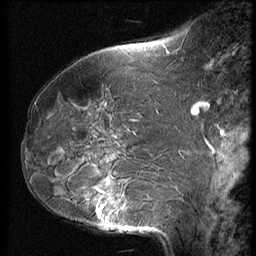
Breast MRI (dynamic contrast-enhanced), one sagittal slice; position 25 of 62 along the scan axis; 3 images stored at this slice position (order not interpretable as contrast timing); 1.5 T; TE 4.2 ms, TR 9 ms; 256 × 256 image matrix, field of view 180 × 180 mm. Patient: female, 50 years. Case-level facts recorded for this patient, not image findings: setting: breast cancer imaged before/during neoadjuvant chemotherapy; receptor status: HR-positive, HER2-negative.
Structures marked on this image (semi-automatically segmented with operator editing):
- analysis volume of interest (the breast-tissue region the enhancement analysis was run in; not a lesion): bounding box [x1, y1, x2, y2] px = [59, 125, 139, 235]
- tumour enhancement mask (voxels above the 140 % enhancement threshold inside the analysis volume of interest): [97, 209, 103, 219]